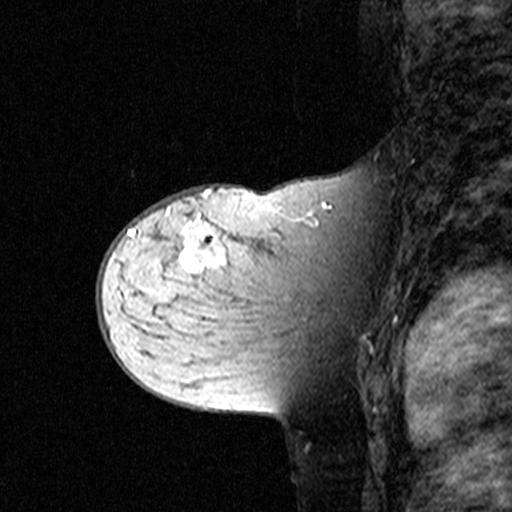
Breast MRI (dynamic contrast-enhanced), one sagittal slice; dynamic contrast-enhanced study with each time point stored as its own series, time point 2 of 3 at this slice position (early post-contrast, ordered by acquisition time); 1.5 T; TE 4.5 ms, TR 11 ms; 512 × 512 image matrix. Female patient, age 44 years. Case-level facts recorded for this patient, not image findings: setting: breast cancer imaged before/during neoadjuvant chemotherapy; receptor status: triple-negative.
Outlined on this slice (semi-automatically segmented with operator editing):
- analysis volume of interest (the breast-tissue region the enhancement analysis was run in; not a lesion): bounding box <142,208,349,363> (left, top, right, bottom; pixels)
- tumour enhancement mask (voxels above the 90 % enhancement threshold inside the analysis volume of interest): <181,212,314,272>